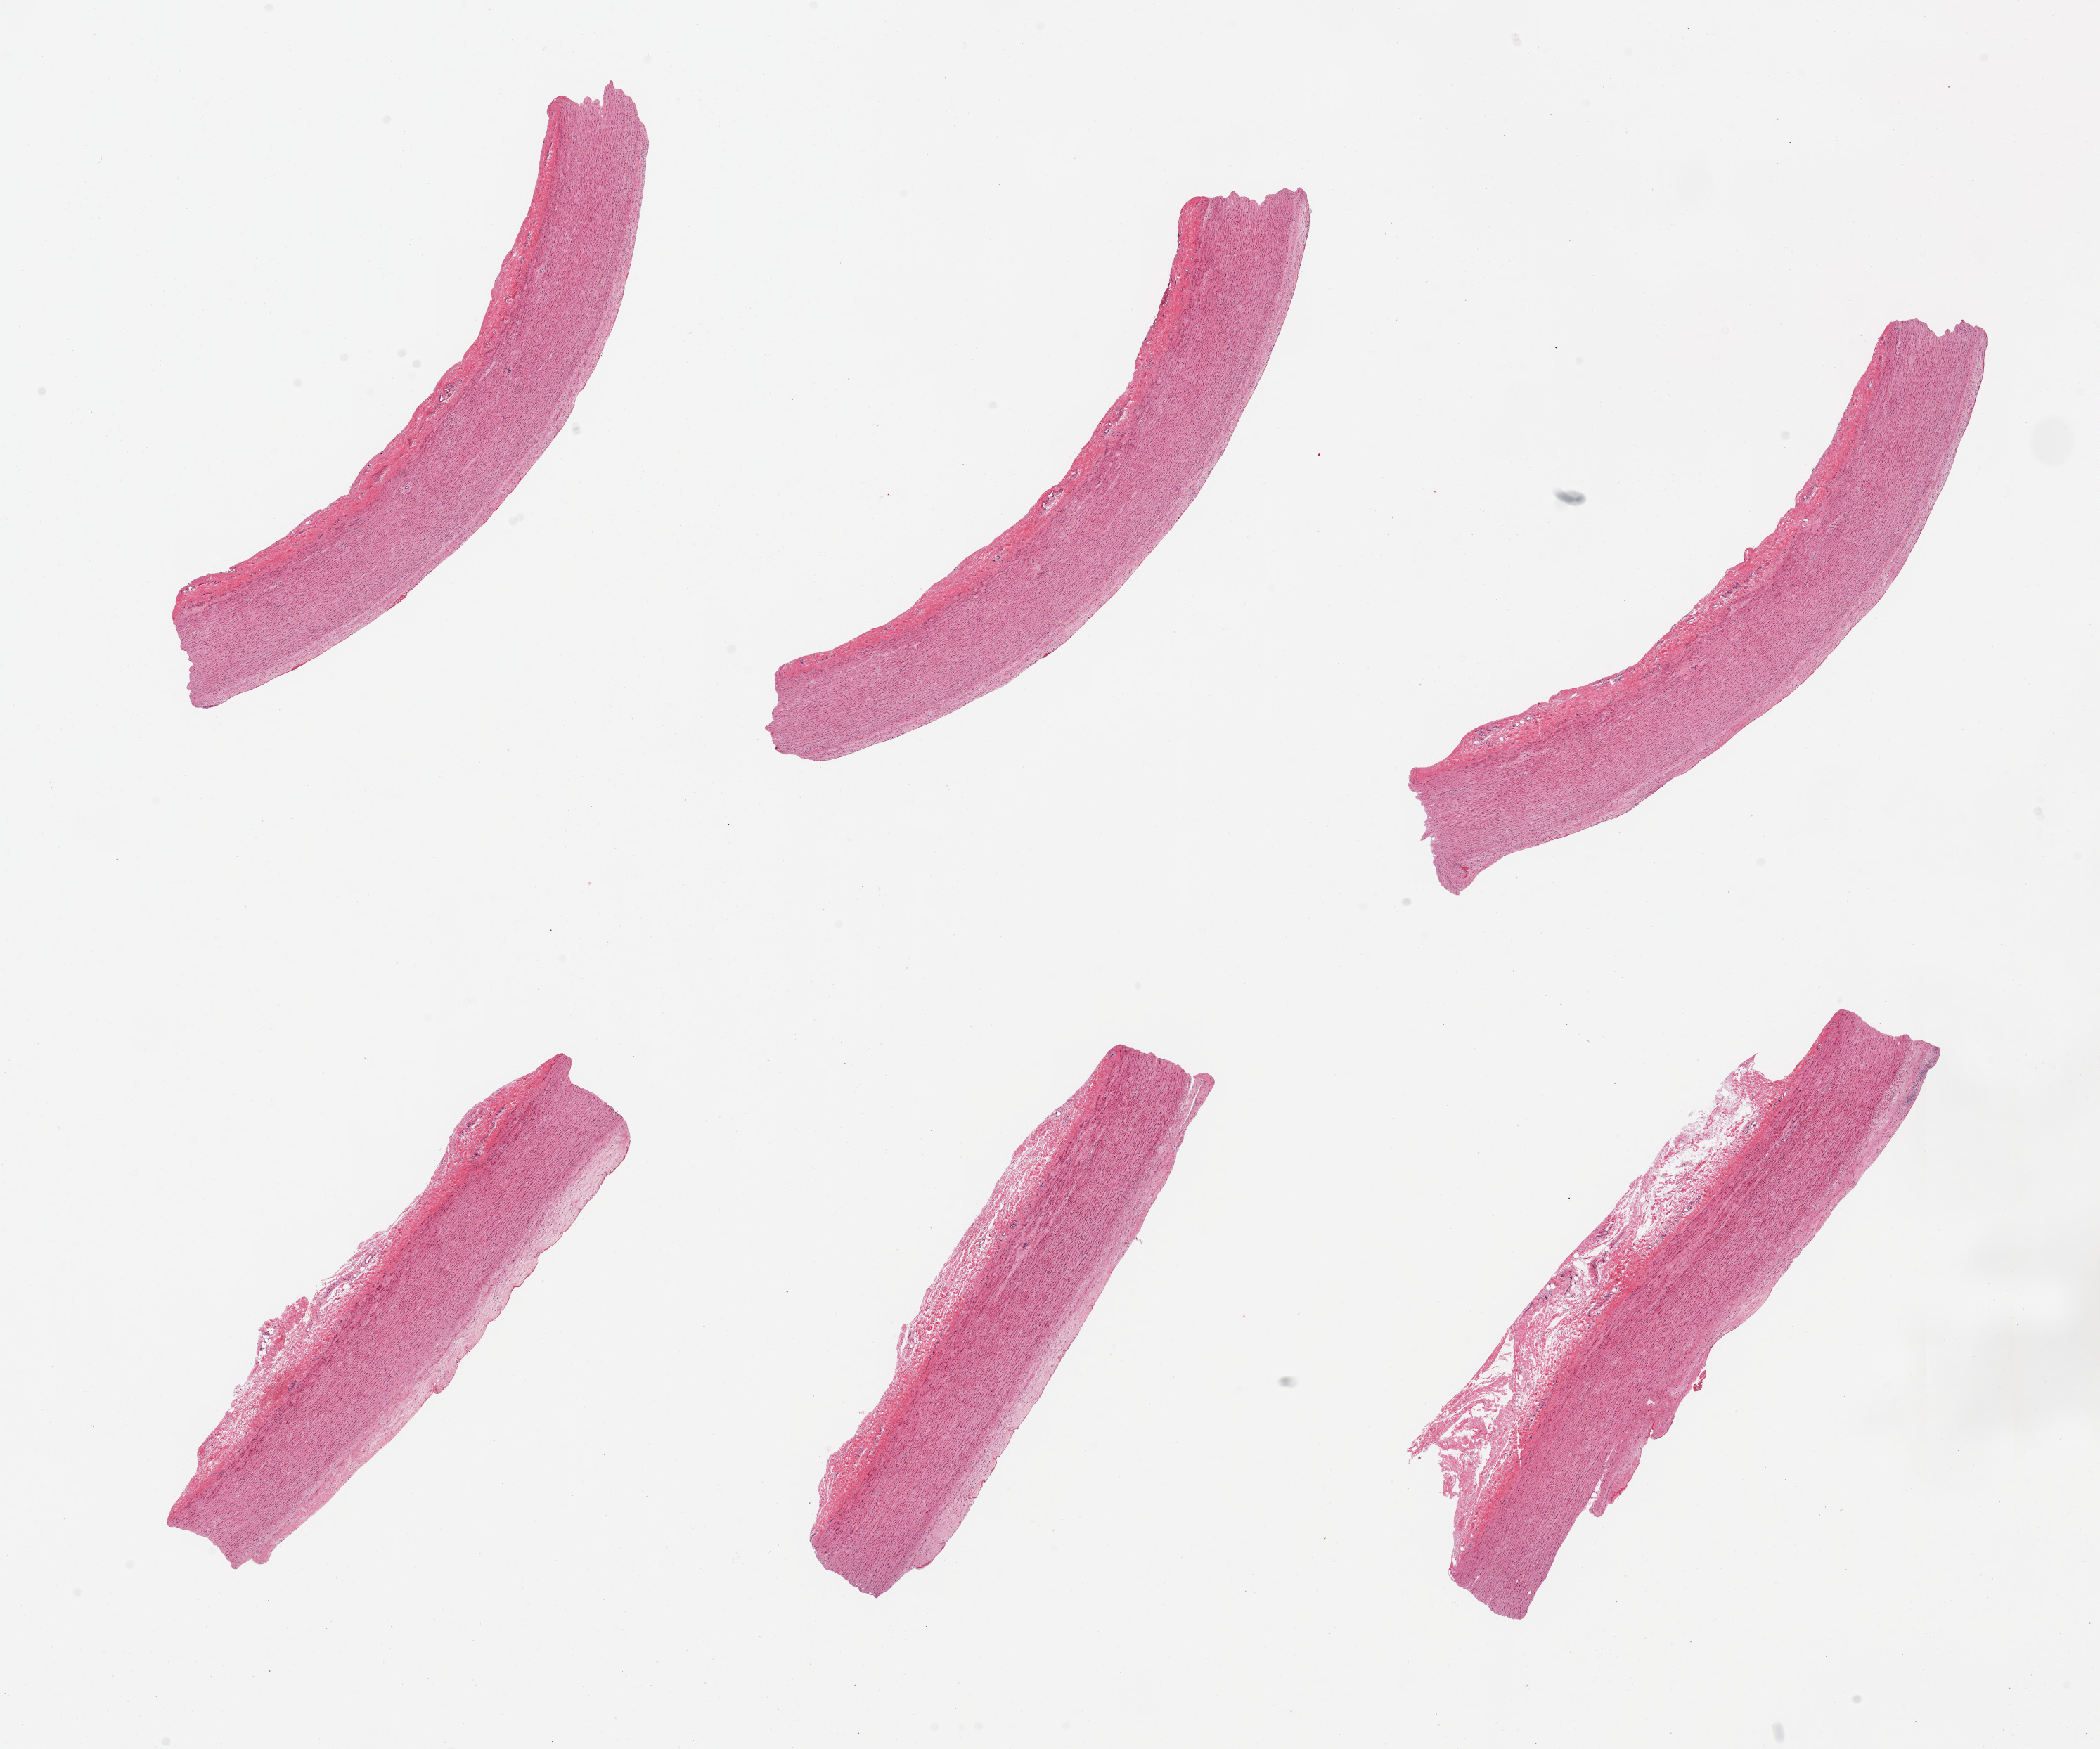
Digitized H&E-stained section, brightfield — a low-resolution overview of the entire scanned area, about 23.6 x 19.7 mm (from a 20x scan); PAXgene-fixed, paraffin-embedded tissue; section of aorta (target tissue); tissue donor sample. Donor: male.
Review note (as recorded): 6 pieces; 3 of 6 have untrimmed adventitia up to 0.5mm thick.